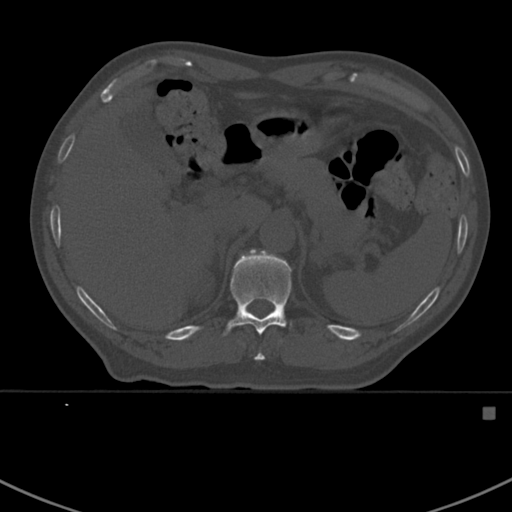
CT including the spine, one axial slice; position 348 of 412 along the scan axis; reconstruction kernel Br40s; 120 kVp; bone window (W 1800 / L 400 HU); 1.5 mm slice thickness; 512 × 512 image matrix, field of view 358 × 358 mm. Male patient, age 59 years. Case-level facts recorded for this patient, not image findings: primary cancer: prostate.
Structures marked on this image (semi-automatically segmented with operator editing):
- T10 vertebra: bounding box <255,352,264,361> (left, top, right, bottom; pixels)
- T11 vertebra: <222,249,293,336>